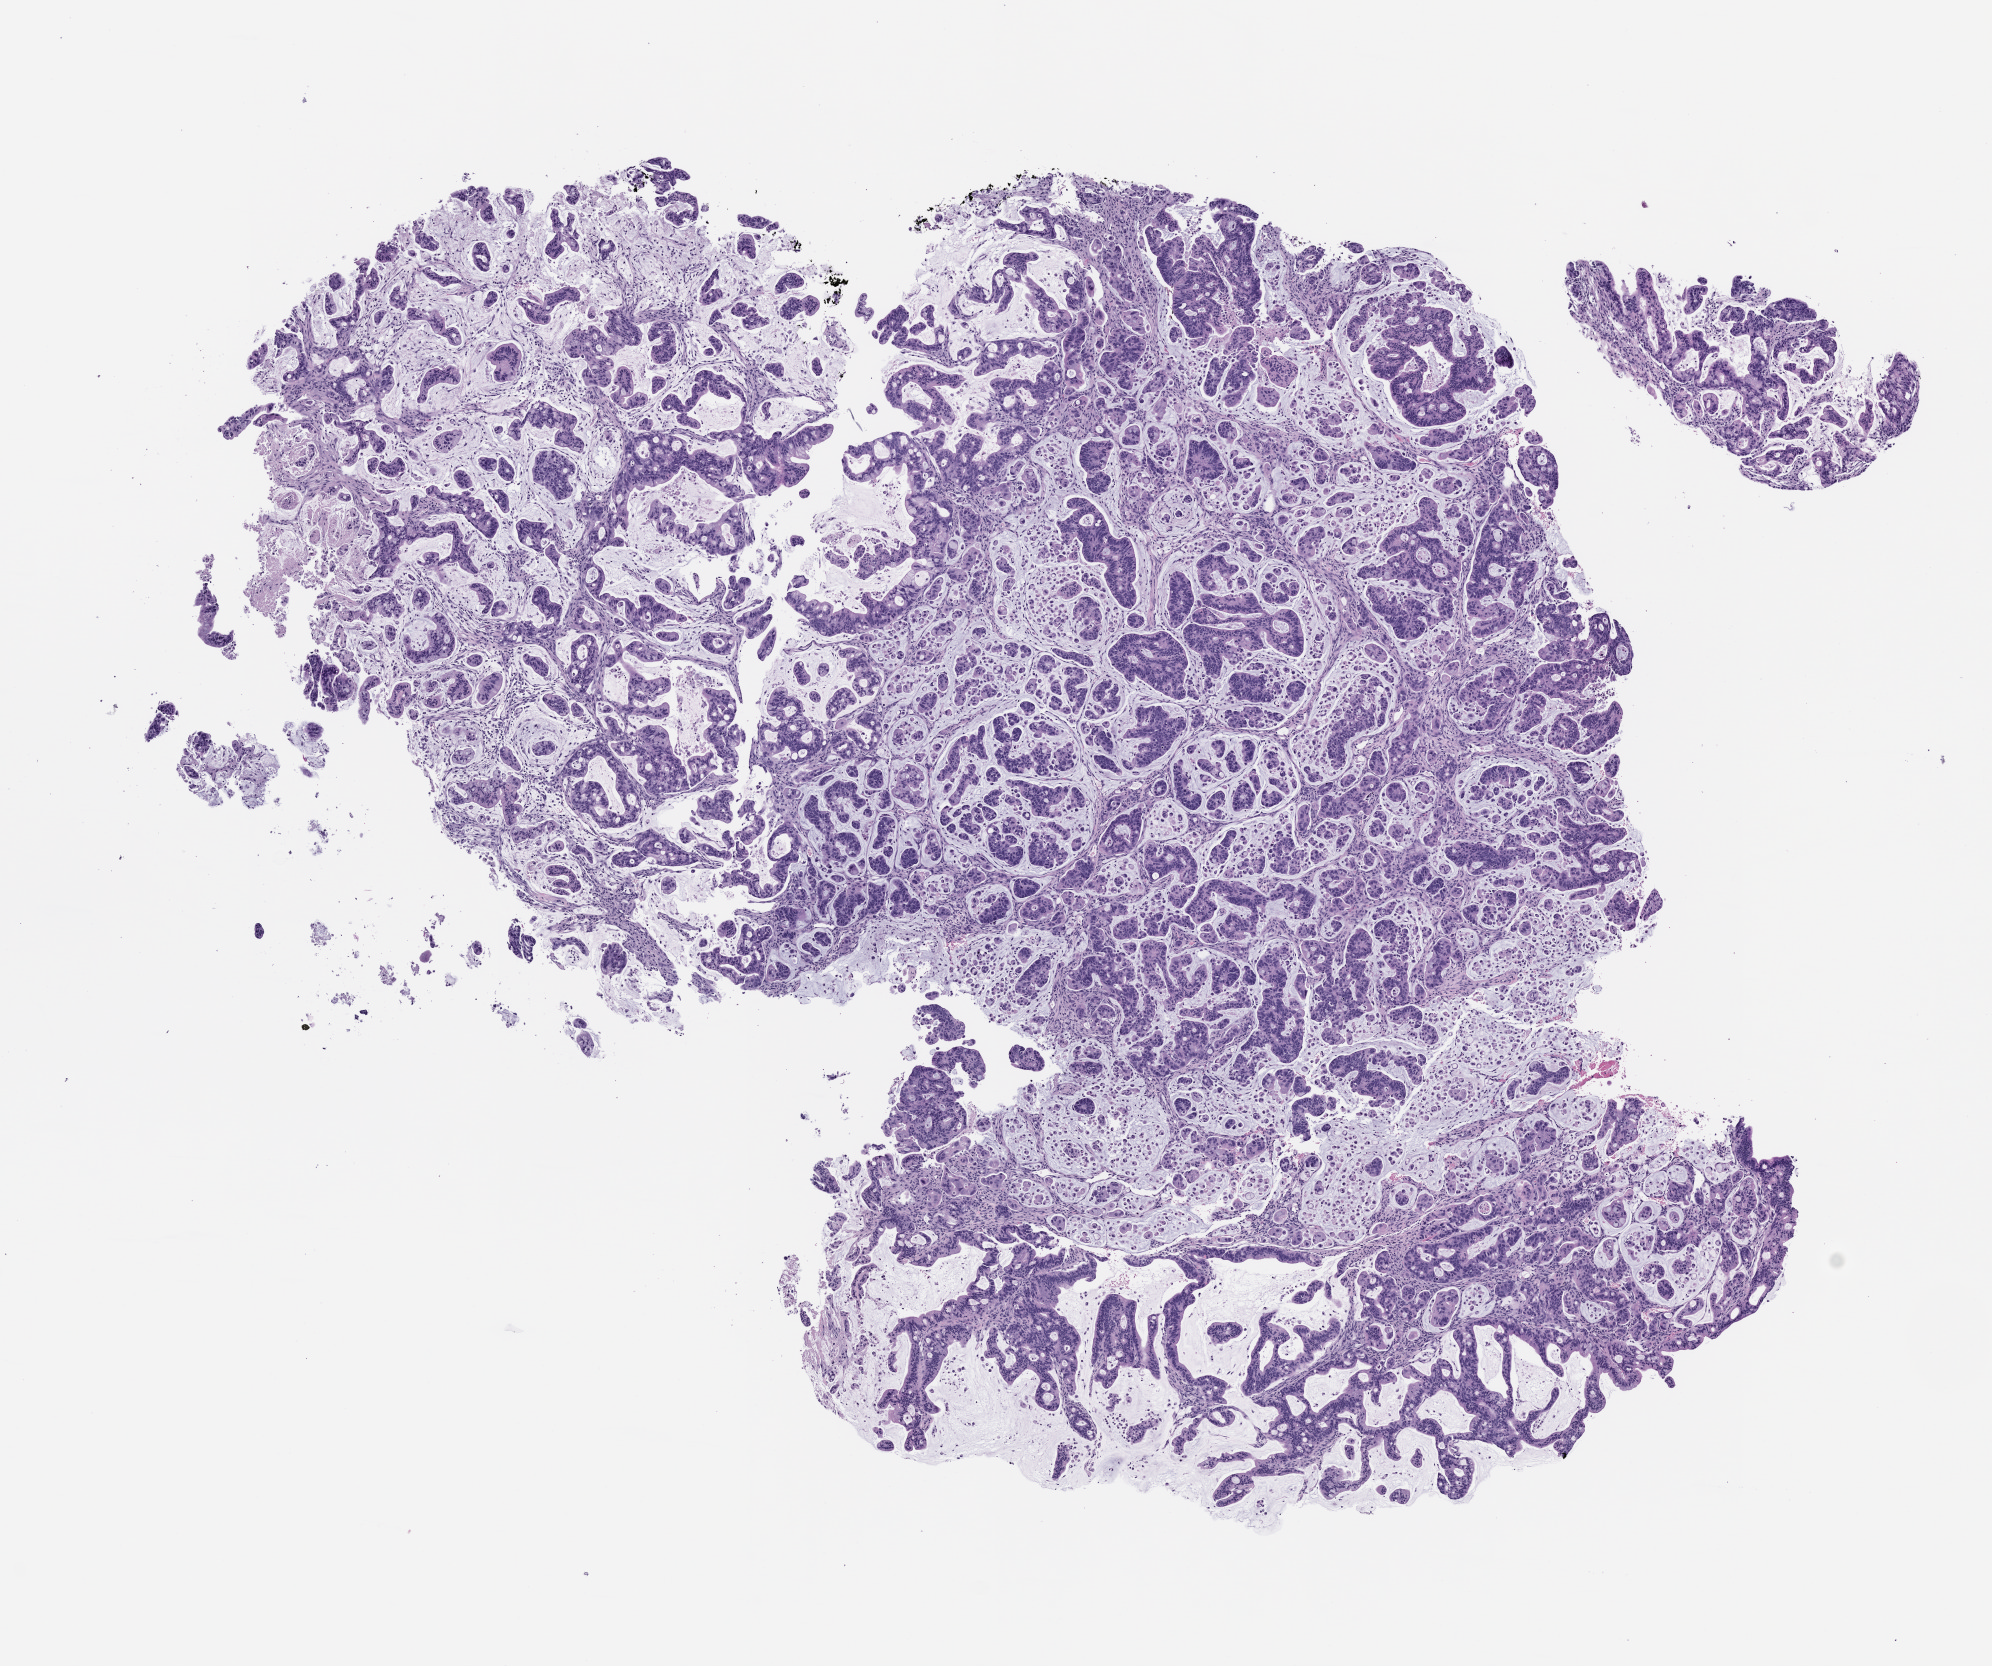
Hematoxylin and eosin (H&E) whole-slide image of a patient-derived xenograft (PDX) tumor grown in a mouse, passage 0 — whole scanned area (about 8.0 x 6.7 mm) shown as a low-resolution overview; formalin-fixed paraffin-embedded section; originating tumor site category: colon.
Originating patient diagnosis: Colon Adenocarcinoma.